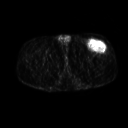
FDG PET of an extremity soft-tissue mass (from a PET/CT study), one axial slice. Slice 250 of 267 in the series (ordered by position). 3.27 mm slice thickness. 128 × 128 image matrix. Male patient, age 64 years. Case-level facts recorded for this patient, not image findings: histological type: extraskeletal osteosarcoma; grade: high; site of the primary tumour: thigh.
Annotated regions visible in this slice (expert contour drawn on MRI and transferred to this co-registered scan by the dataset authors):
- gross tumour volume (mass): bounding box (x1, y1, x2, y2) in pixels: (89, 42, 106, 52)